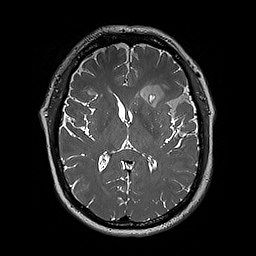
Brain MRI from a brain-tumour surgery series, one axial slice; position 106 of 192 along the scan axis; 1 mm slice thickness; 256 × 256 image matrix, field of view 250 × 250 mm. From the clinical record (not read from this slice): histopathology: Oligodendroglioma; WHO grade: 3; IDH mutation: yes; tumour location: Left Sylvian Fissure (Temporal).
Outlined on this slice (expert manual segmentation):
- tumour: bounding box (x1, y1, x2, y2) in pixels: (148, 81, 197, 119)